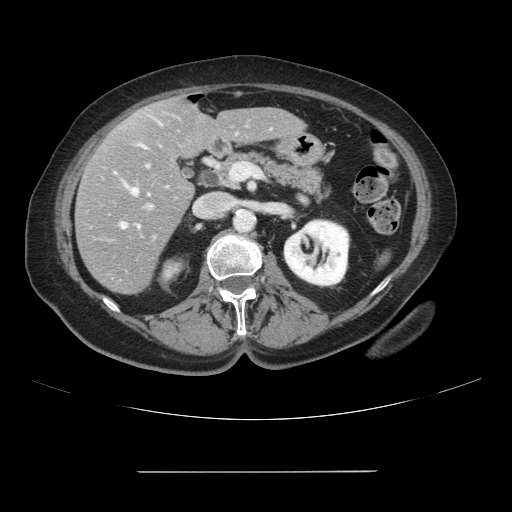
Contrast-enhanced abdominal CT, one axial slice. Slice 42 of 111 in the series (ordered by position). Intravenous contrast given. Soft-tissue window (W 400 / L 40 HU). 512 × 512 image matrix, field of view 400 × 400 mm. Female patient, age 74 years. Case-level facts recorded for this patient, not image findings: diagnosis: colorectal cancer liver metastases, imaged before liver resection; multiple liver metastases: yes; largest metastasis: 1.1 cm.
Structures marked on this image (manually delineated by an expert):
- hepatic veins: bounding box (x1, y1, x2, y2) in pixels: (121, 188, 139, 228)
- liver: (75, 98, 304, 294)
- planned liver remnant (the part of the liver to remain after resection): (141, 98, 304, 158)
- portal vein (with intrahepatic branches): (147, 205, 151, 208)